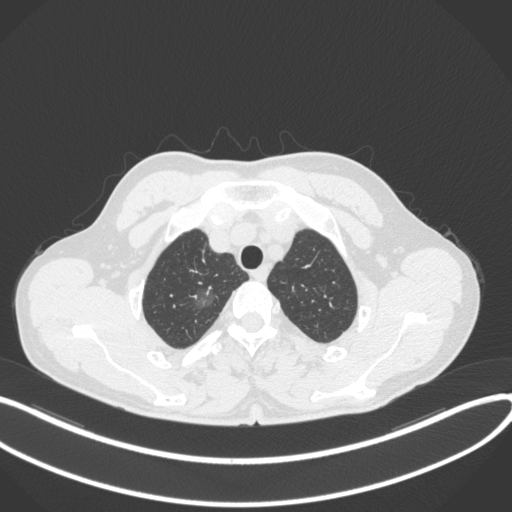
Chest CT, one axial slice. Position 326 of 407 along the scan axis. Reconstruction kernel B31f. 120 kVp. Lung window (W 1500 / L -600 HU). 1 mm slice thickness. 512 × 512 image matrix, field of view 400 × 400 mm. Male patient, age 58 years. Case-level facts recorded for this patient, not image findings: clinical TNM (as recorded): T1c N0 M0; histopathological grade: G1-2.
Outlined on this slice (bounding box drawn by a radiologist):
- lung tumour (recorded histology: adenocarcinoma): bounding box <191,285,216,312> (left, top, right, bottom; pixels)